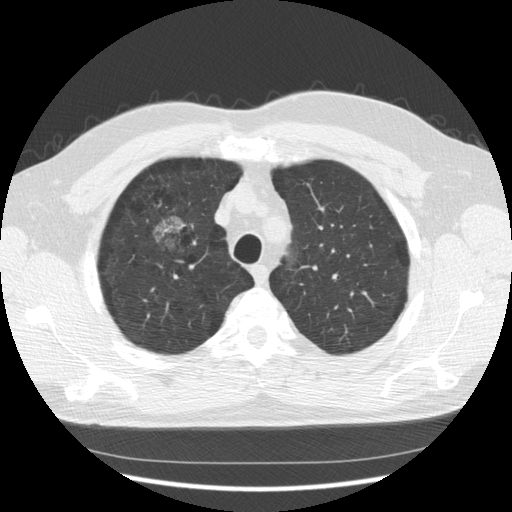
Chest CT (low-dose screening protocol), one axial image, third screening round (two years after baseline), lung window (W 1500 / L -600 HU), 2.5 mm slice thickness, standard (soft-tissue) reconstruction kernel (STANDARD), 140 kVp. Male participant, aged 60 years at enrolment. Former smoker at enrolment.
• Lesion marked by an expert reader, bounding box (x1, y1, x2, y2) in pixels: (142, 205, 199, 266).
• Reader record for this screening exam (exam-level; its link to the box is not recorded): non-calcified nodule or mass ≥4 mm, right upper lobe, poorly defined margins, mixed attenuation, pre-existing on the prior screen: yes; interval growth: yes.
• Lung cancer was diagnosed 121 days after this screen: papillary adenocarcinoma, NOS, right upper lobe, moderately differentiated (G2), stage IB (AJCC 6th edition), 32 mm at pathology.